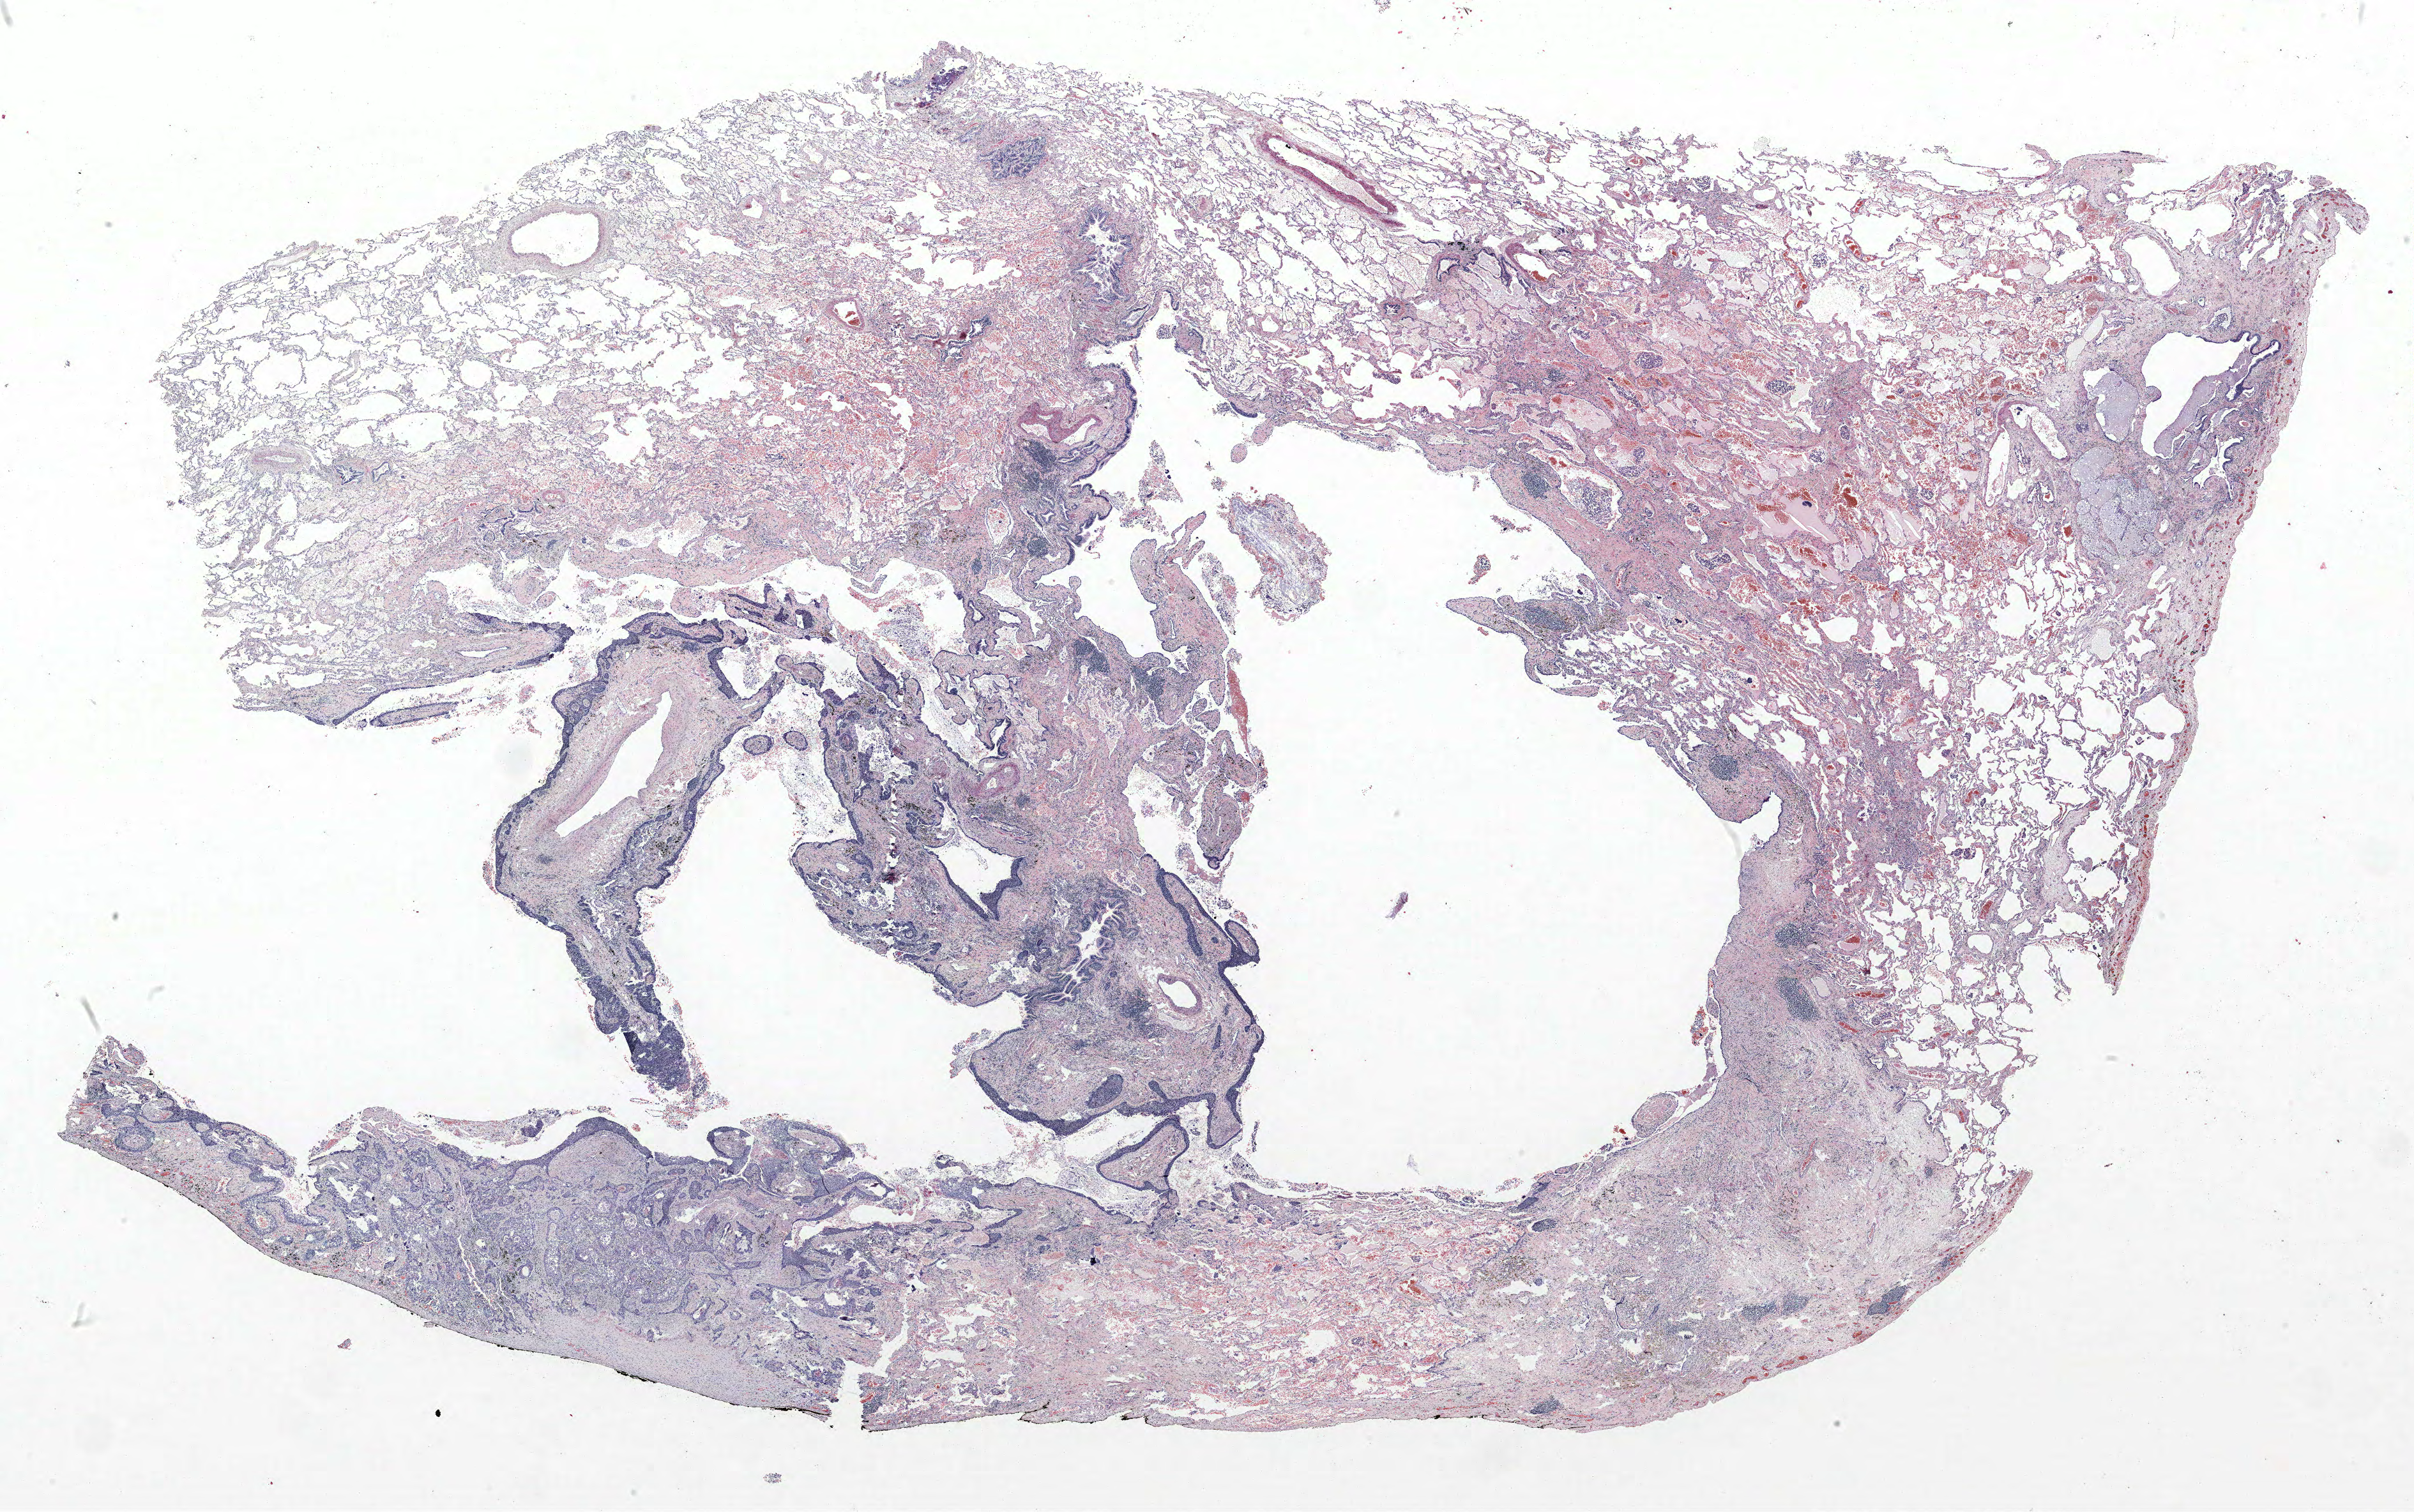
Whole-slide histology image, Hematoxylin and eosin (H&E) stained, low-resolution overview of the scanned area, about 30.2 x 18.9 mm (slide scanned at 40x); formalin-fixed paraffin-embedded (FFPE) section; lung. Male, age 55 at enrolment. Current smoker at enrolment. Grade: moderately differentiated (G2).
Participant's lung-cancer diagnosis: Adenocarcinoma, NOS. Stage (AJCC 6th edition): IB. Tumour size (pathology): 75 mm. Primary tumour location (clinical record): right lower lobe. Note: participant had 2 primary lung cancers recorded; fields above describe the first.